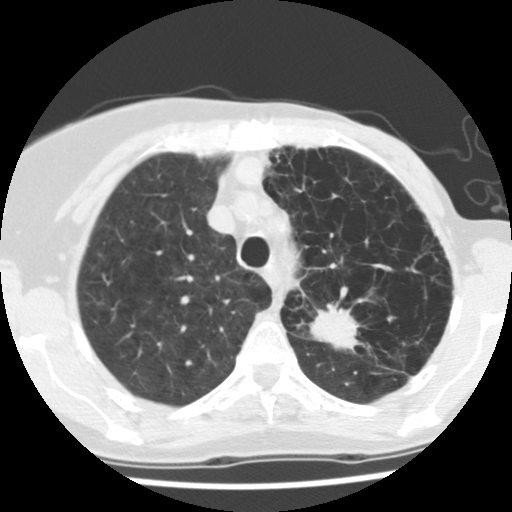
Low-dose screening chest CT, axial slice; baseline screening round; lung window (W 1500 / L -600 HU); 2.5 mm slice thickness; standard (soft-tissue) reconstruction kernel (STANDARD); 140 kVp. Female, age 67 years at enrolment. Current smoker at enrolment.
- Lesion marked by an expert reader, bounding box (x1, y1, x2, y2) in pixels: (298, 288, 383, 365).
- The screening reader recorded 2 non-calcified nodules or masses ≥4 mm on this exam (left upper lobe, left lower lobe); which of them this box marks is not recorded.
- Official screen result: positive, change unspecified: nodule(s) >= 4 mm or enlarging nodule(s), mass(es), or other non-specific abnormalities suspicious for lung cancer.
- Lung cancer was diagnosed 109 days after this screen: adenocarcinoma, NOS, left upper lobe, poorly differentiated (G3), stage IIB (AJCC 6th edition), 45 mm at pathology.